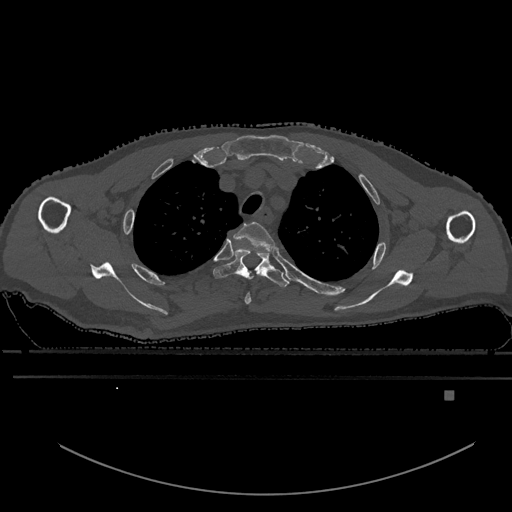
CT including the spine, one axial slice; slice 466 of 969 in the series (ordered by position); bone window (W 1800 / L 400 HU); 512 × 512 image matrix, field of view 456 × 456 mm. Male patient, age 82 years. Case-level facts recorded for this patient, not image findings: primary cancer: prostate.
Annotated regions visible in this slice (semi-automatic segmentation, software-assisted and operator-edited):
- T2 vertebra: bounding box (x1, y1, x2, y2) in pixels: (234, 221, 275, 305)
- T3 vertebra: (214, 249, 289, 287)